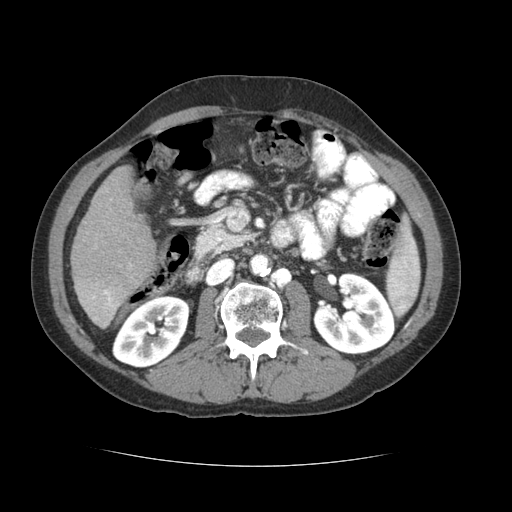
Contrast-enhanced abdominal CT (liver protocol), one axial slice. Slice 22 of 69 in the series (ordered by position). Soft-tissue window (W 400 / L 40 HU). 2.5 mm slice thickness. 512 × 512 image matrix, field of view 360 × 360 mm. From the clinical record (not read from this slice): diagnosis: hepatocellular carcinoma (patient treated with transarterial chemoembolisation; whether this scan precedes or follows treatment is not stated here); TNM stage (as recorded): Stage-II; Child-Pugh class: B.
Annotated regions visible in this slice (semi-automatic segmentation, software-assisted and operator-edited):
- liver parenchyma outside the tumour (the mass and vessels are separate outlines, so this box may not span the whole liver): bounding box <70,166,156,328> (left, top, right, bottom; pixels)
- liver vessels: <87,264,131,325>